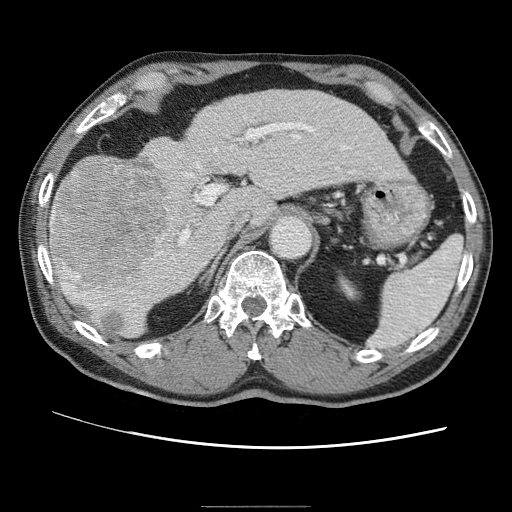
Contrast-enhanced abdominal CT (liver protocol), one axial slice; position 35 of 75 along the scan axis; reconstruction kernel STANDARD; 120 kVp; one of 2 acquisitions stored at this slice position; soft-tissue window (W 400 / L 40 HU); 512 × 512 image matrix. Case-level facts recorded for this patient, not image findings: diagnosis: hepatocellular carcinoma (patient treated with transarterial chemoembolisation; whether this scan precedes or follows treatment is not stated here); TNM stage (as recorded): Stage-II; Child-Pugh class: A; tumour differentiation: well differentiated; tumour nodularity: multinodular.
Structures marked on this image (semi-automatic segmentation, software-assisted and operator-edited):
- liver parenchyma outside the tumour (the mass and vessels are separate outlines, so this box may not span the whole liver): box from (x=50, y=90) to (x=406, y=336) px
- mass: (x=51, y=163)–(x=167, y=300)
- liver vessels: (x=61, y=126)–(x=350, y=305)